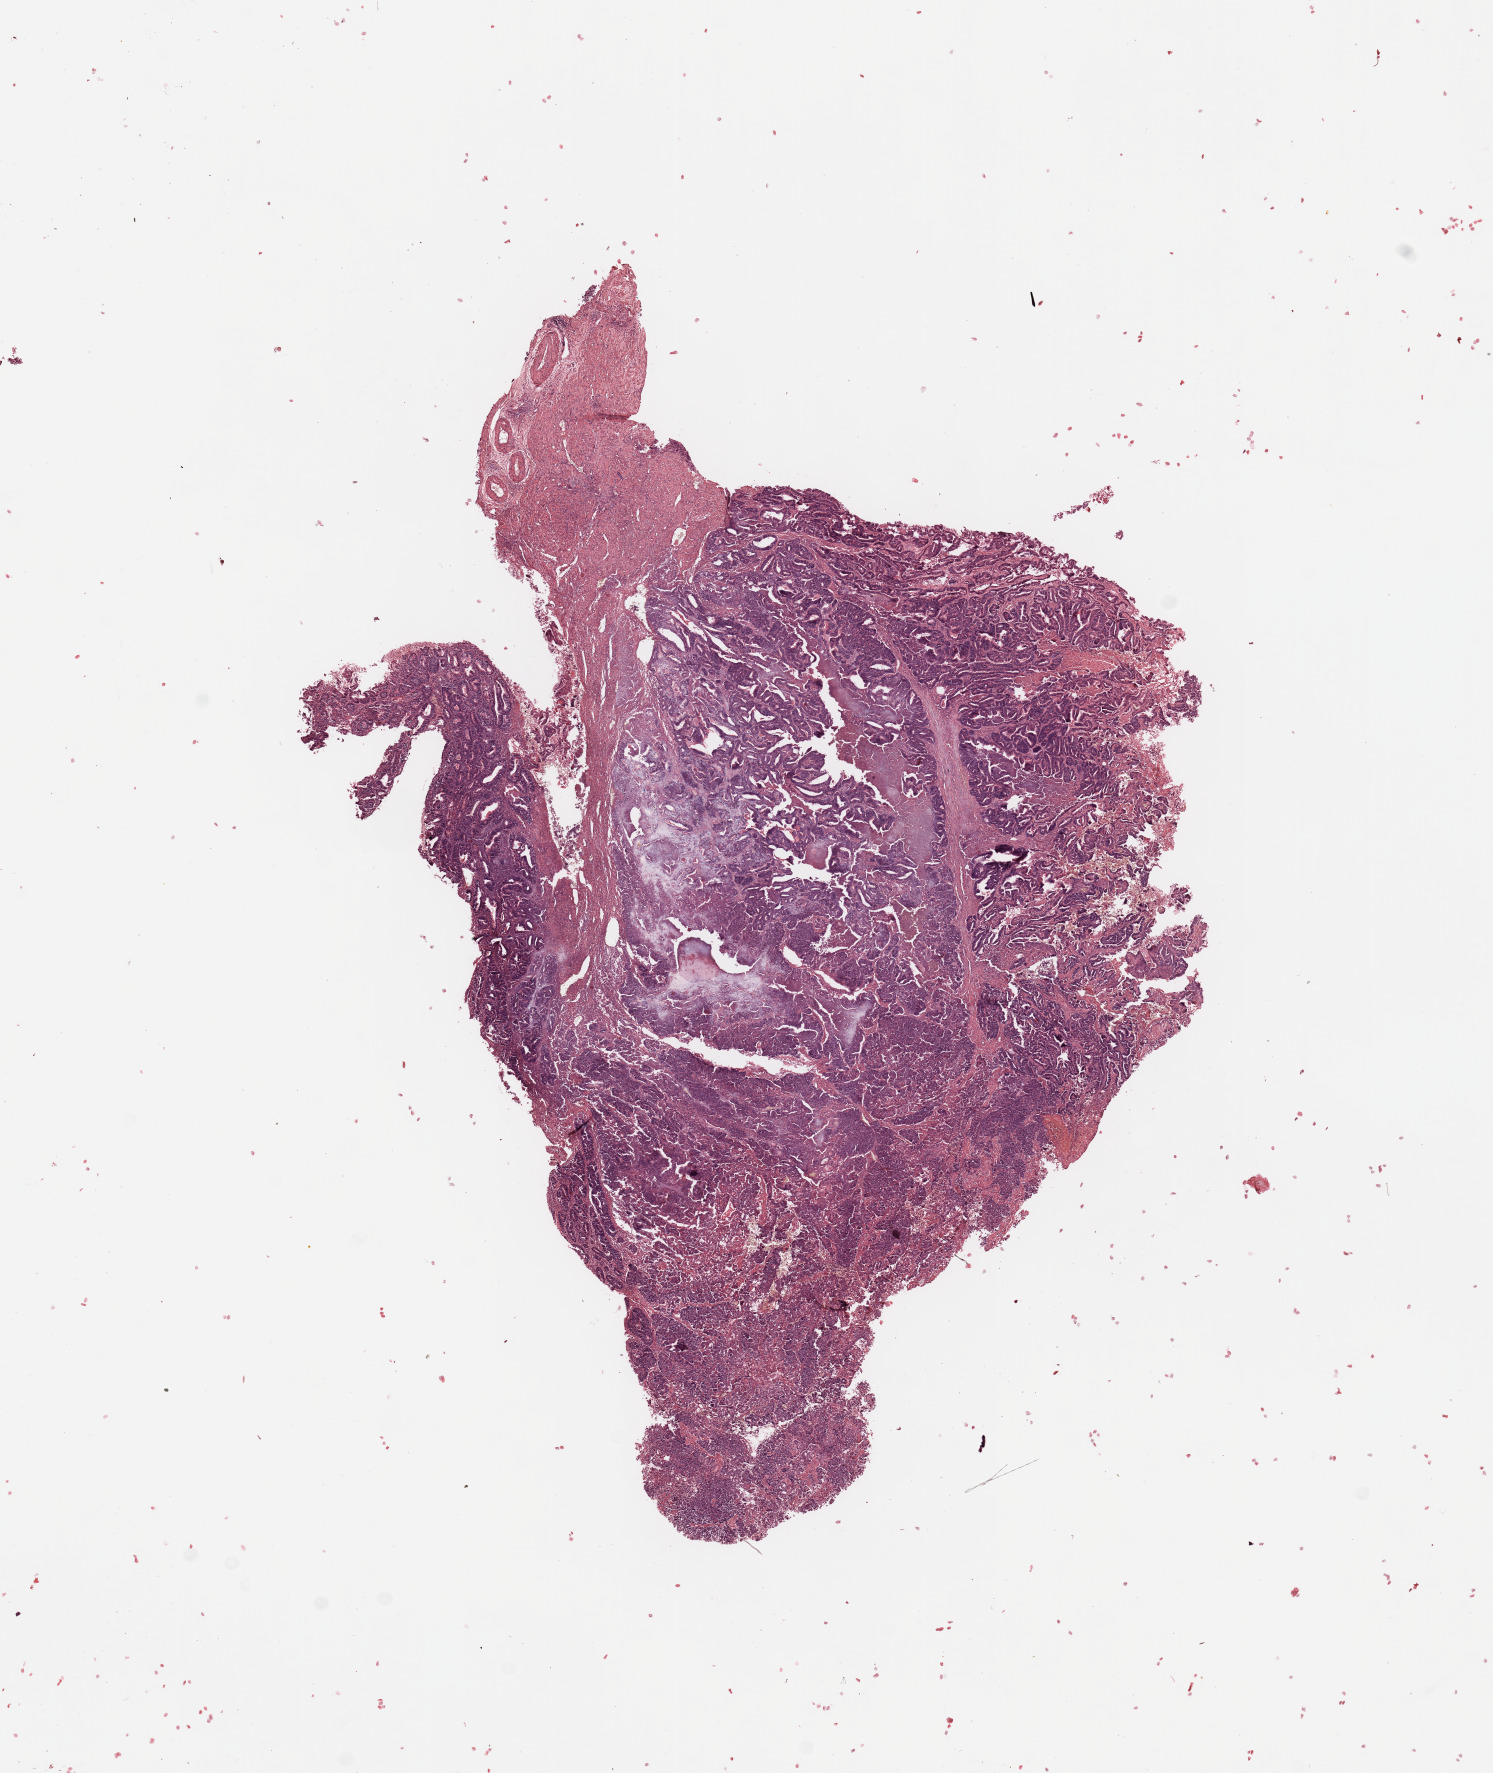
Digitized H&E tissue section (whole slide), a low-resolution overview of the entire scanned area, about 11.8 x 14.0 mm (from a 20x scan). Tumour tissue sample, uterus. Female, 68 y/o. Histologic grade: G2 (moderately differentiated).
- AJCC pathologic stage: III
- histologic diagnosis: Endometrioid adenocarcinoma, NOS